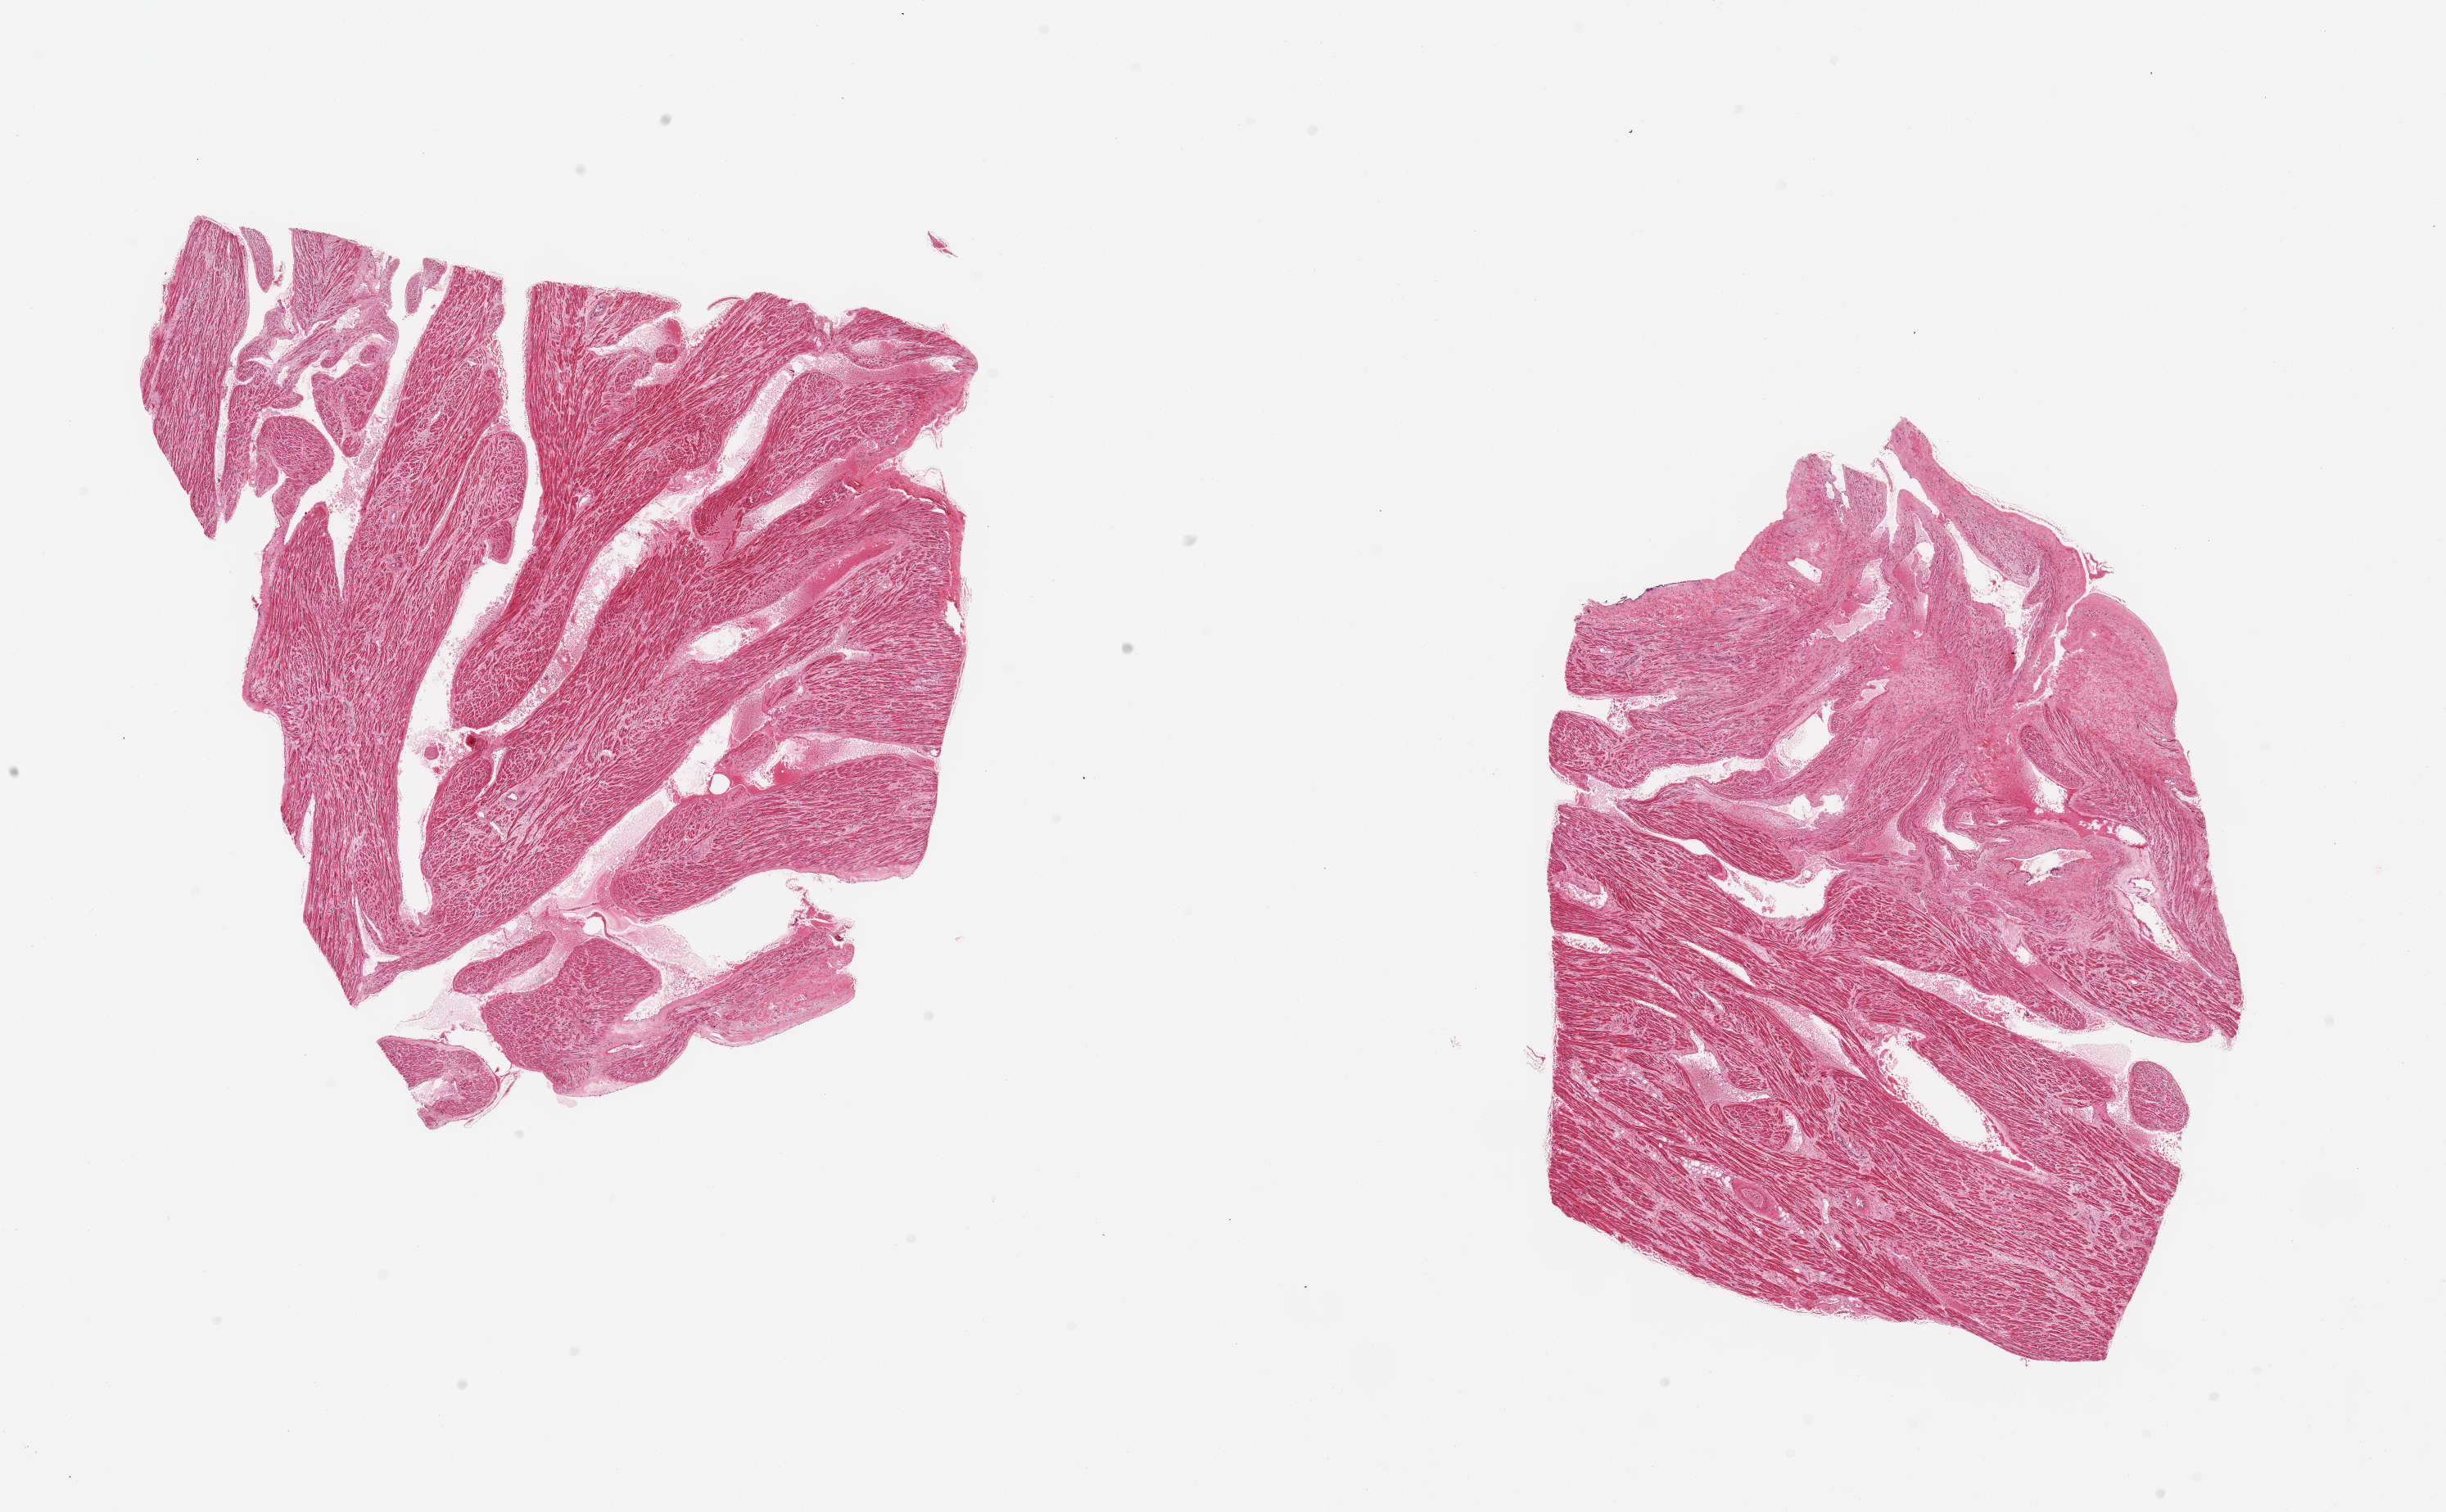
Digitized H&E-stained section, low-resolution overview of the scanned area, about 23.6 x 14.6 mm (acquisition: 20x scan); PAXgene-fixed paraffin-embedded (PFPE) section; sampled site (target tissue): auricular appendage; tissue donor sample. Donor sex: male.
• pathologist's review note for this sample: 2 pieces, no abnormalities